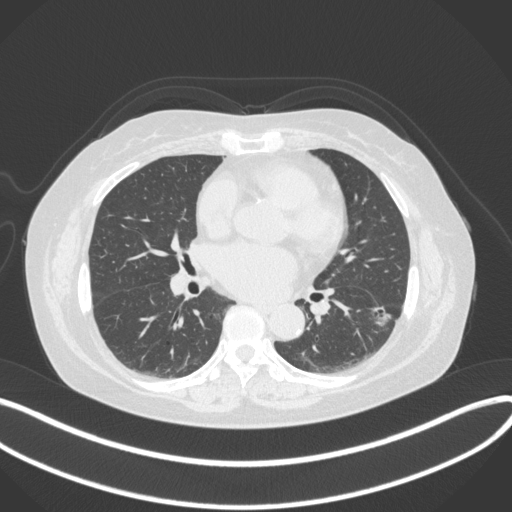
Chest CT, one axial slice; slice 174 of 373 in the series (ordered by position); lung window (W 1500 / L -600 HU); 1 mm slice thickness; 512 × 512 image matrix, field of view 400 × 400 mm. Patient: female, 67 years. From the clinical record (not read from this slice): clinical TNM (as recorded): T1c N0 M0; histopathological grade: G2.
Annotated regions visible in this slice (bounding box drawn by a radiologist):
- lung tumour (recorded histology: adenocarcinoma): bounding box [x1, y1, x2, y2] px = [366, 301, 393, 328]